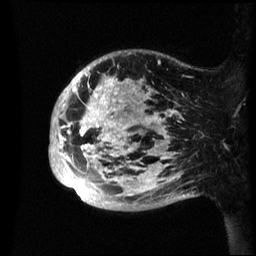
Breast MRI (dynamic contrast-enhanced), one sagittal slice. Slice 12 of 60 in the series (ordered by position). Dynamic contrast-enhanced series, image 2 of 3 at this slice position (ordered by acquisition). 1.5 T. TE 4.2 ms, TR 8.4 ms. 256 × 256 image matrix, field of view 230 × 230 mm. Female patient, age 48 years.
Annotated regions visible in this slice (semi-automatic segmentation, software-assisted and operator-edited):
- analysis volume of interest (the breast-tissue region the enhancement analysis was run in; not a lesion): bounding box <49,50,195,211> (left, top, right, bottom; pixels)
- tumour enhancement mask (voxels above the 70 % enhancement threshold inside the analysis volume of interest): <49,73,181,196>